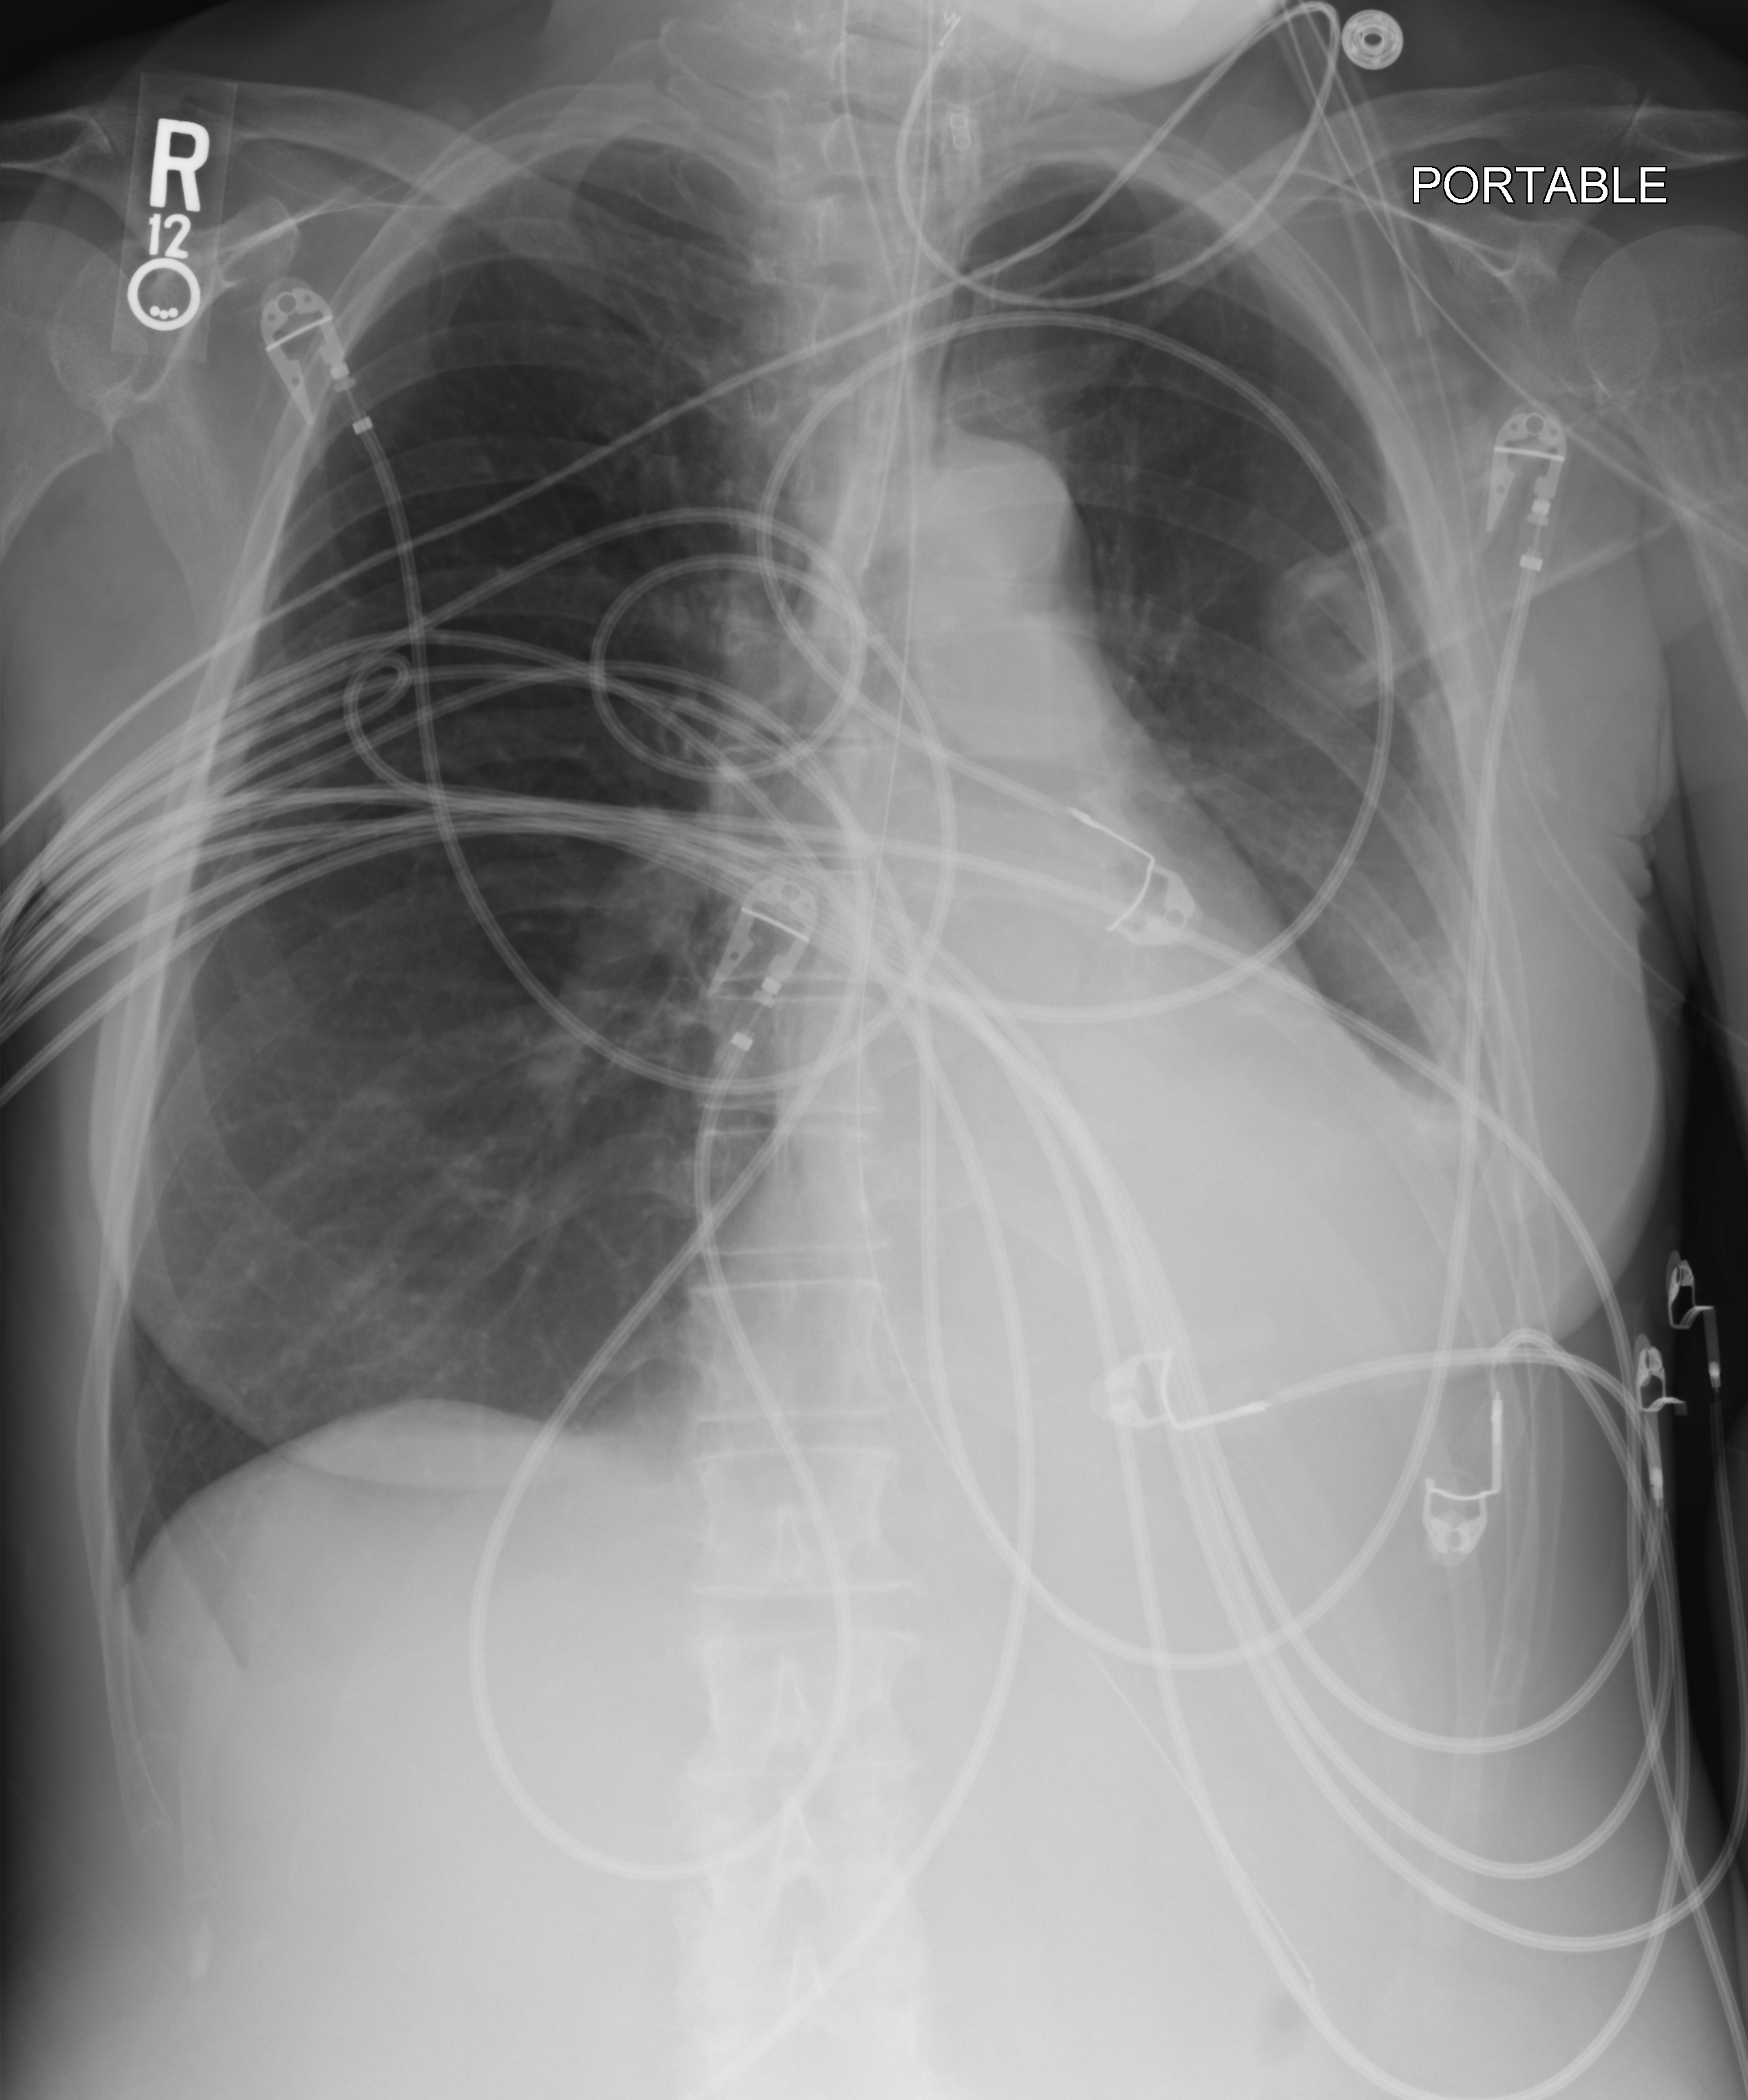
Portable chest radiograph, anteroposterior (AP) projection. Female patient hospitalised with COVID-19, age 60–74 years.
Hospital-stay facts (about this admission, not read from this image; timing relative to this image not recorded): mechanically ventilated during this hospital stay: yes.